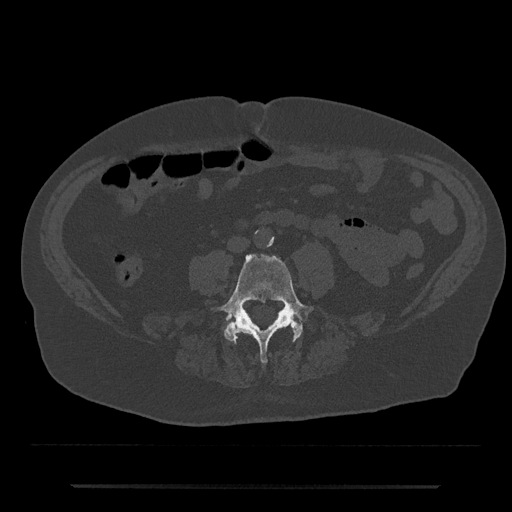
CT including the spine, one axial slice; slice 348 of 797 in the series (ordered by position); reconstruction kernel Br40s/3; bone window (W 1800 / L 400 HU); 0.5 mm slice thickness; 512 × 512 image matrix, field of view 434 × 434 mm. Patient: male, 80 years. From the clinical record (not read from this slice): primary cancer: prostate.
Annotated regions visible in this slice (semi-automatic segmentation, software-assisted and operator-edited):
- L4 vertebra: bounding box [x1, y1, x2, y2] px = [219, 254, 315, 363]
- L5 vertebra: [228, 319, 302, 340]